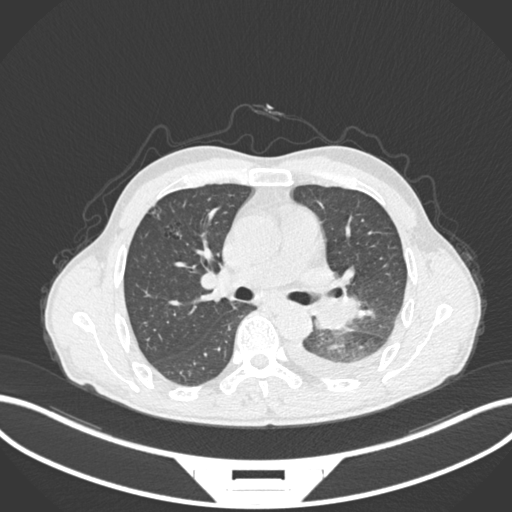
Chest CT, one axial slice; position 149 of 222 along the scan axis; reconstruction kernel B30f; 120 kVp; lung window (W 1500 / L -600 HU); 1 mm slice thickness; 512 × 512 image matrix. Male patient, age 47 years. From the clinical record (not read from this slice): clinical TNM (as recorded): T3 N1 M1c; histopathological grade: G3.
Annotated regions visible in this slice (rectangle marked by the reading radiologist):
- lung tumour (recorded histology: small cell carcinoma): box from (x=308, y=296) to (x=366, y=330) px